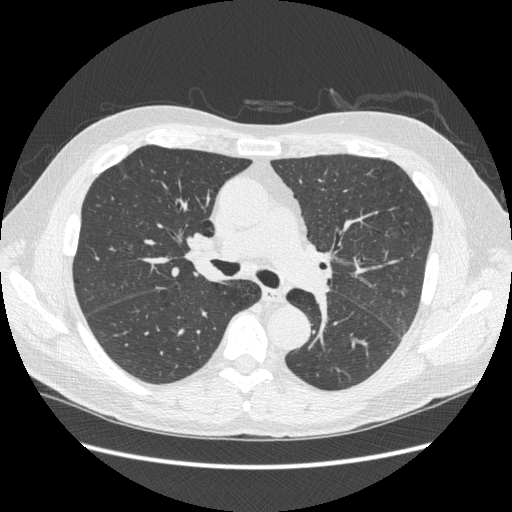
Axial slice from a low-dose chest CT screening exam. Third screening round (two years after baseline). Lung window (W 1500 / L -600 HU). Standard (soft-tissue) reconstruction kernel (STANDARD). 120 kVp. Slice 107 of 258 in the series. 512 × 512 image matrix, field of view 380 × 380 mm. Male, age 59 years at enrolment. Current smoker at enrolment.
Expert reader's lesion annotation, bounding box [x1, y1, x2, y2] px = [179, 225, 230, 267]. The screening reader recorded 2 non-calcified nodules or masses ≥4 mm on this exam; which of them this box marks is not recorded. Later outcome: lung cancer diagnosed 169 days after this screen — squamous cell carcinoma, keratinizing, NOS, right hilum, stage IIIB (AJCC 6th edition).